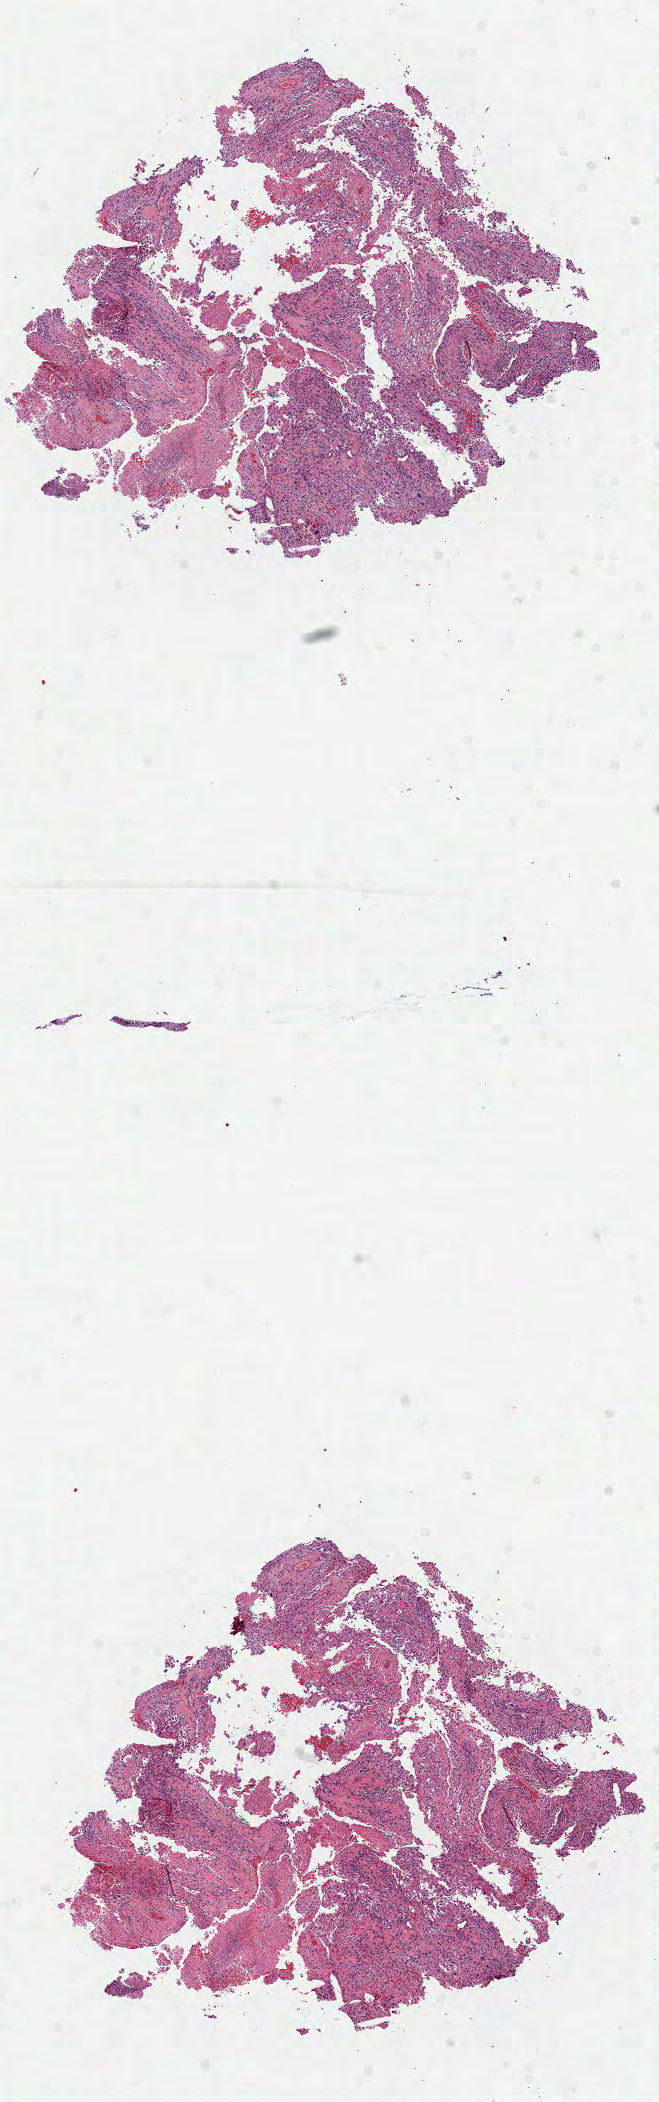
H&E whole-slide image — a low-resolution overview of the entire scanned area, about 5.3 x 17.0 mm, formalin-fixed paraffin-embedded (FFPE) diagnostic section, brain, primary tumour sample. Female, age 63 years at initial diagnosis.
- pathologic diagnosis: Glioblastoma